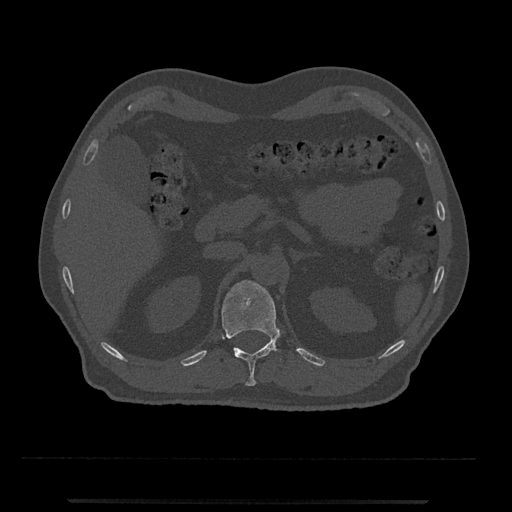
CT including the spine, one axial slice; position 394 of 797 along the scan axis; reconstruction kernel Br40s/3; bone window (W 1800 / L 400 HU); 0.5 mm slice thickness; 512 × 512 image matrix. Patient: male, 63 years. From the clinical record (not read from this slice): primary cancer: prostate.
Outlined on this slice (semi-automatically segmented with operator editing):
- T12 vertebra: box from (x=222, y=280) to (x=281, y=386) px